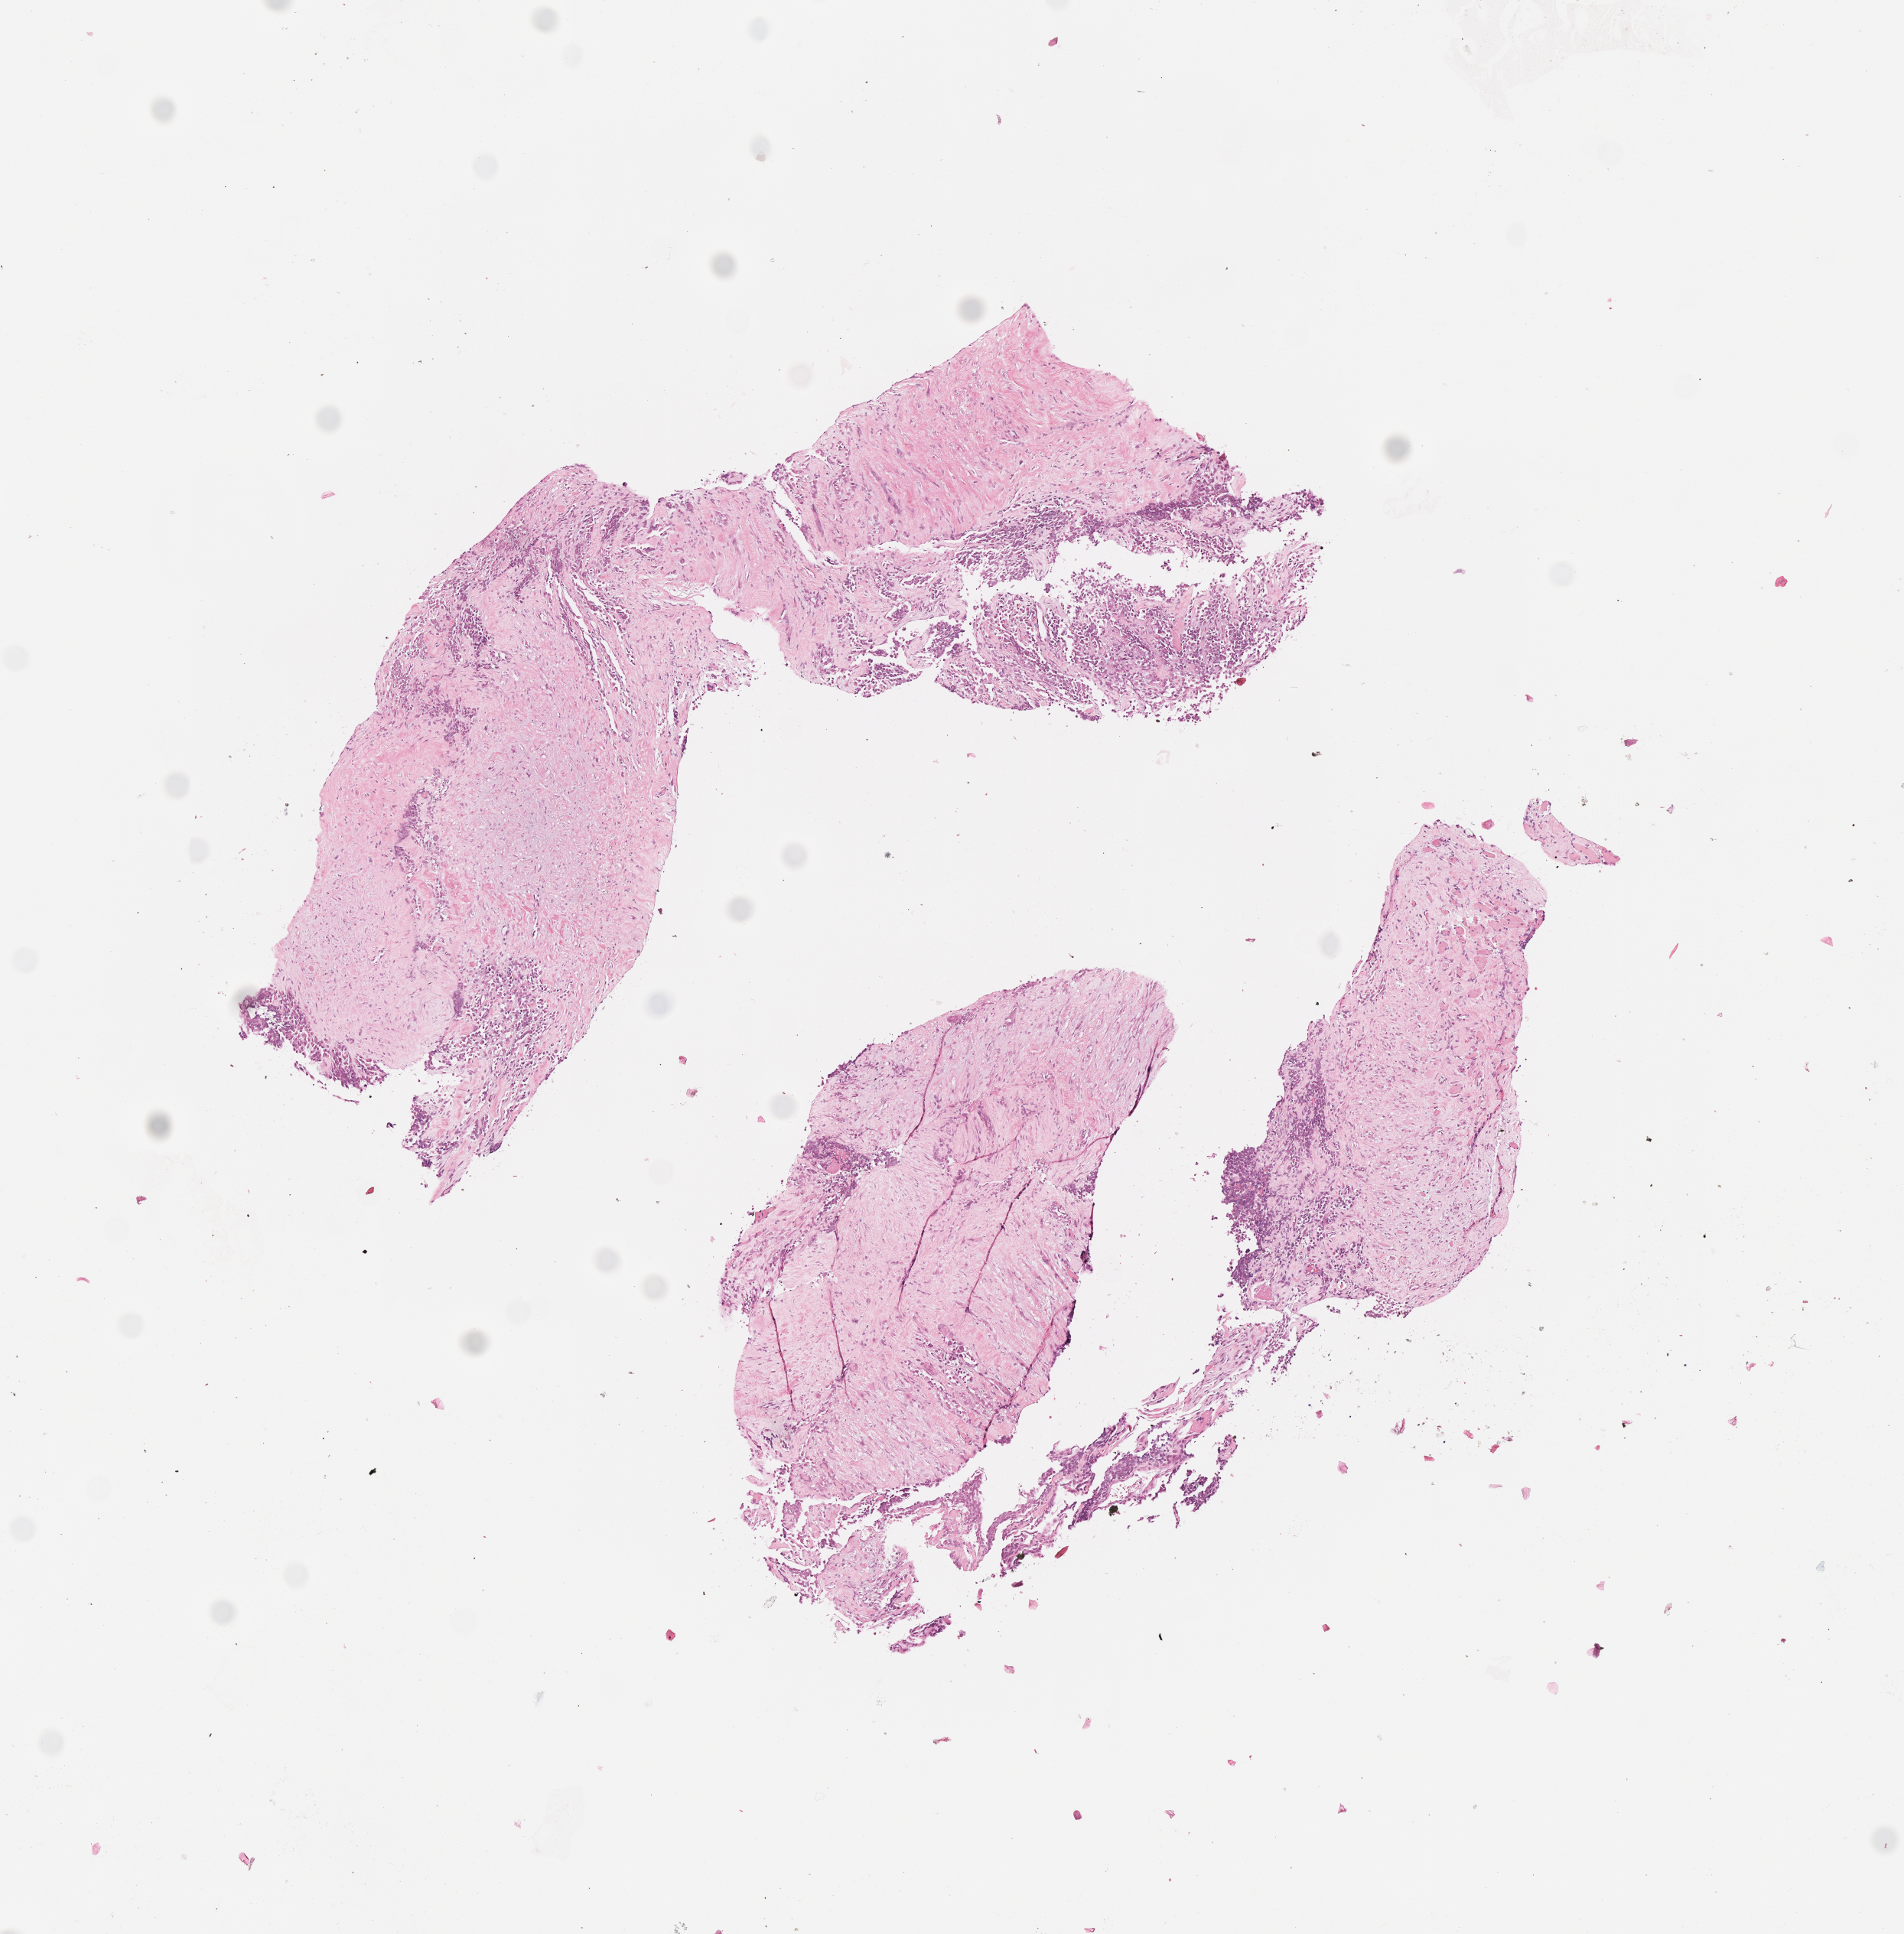
Digitized hematoxylin and eosin (H&E)-stained section of tumor tissue — low-resolution overview of the scanned area, about 5.0 x 5.1 mm. FFPE section. Sample anatomic site: soft tissue, calf-right. Female patient, age at diagnosis 14.0 years.
Diagnosis: rhabdomyosarcoma; histological classification: alveolar rhabdomyosarcoma. Stage (as recorded): 2. Primary site (case record): leg. Metastatic status at presentation (as recorded): non-metastatic (unconfirmed).